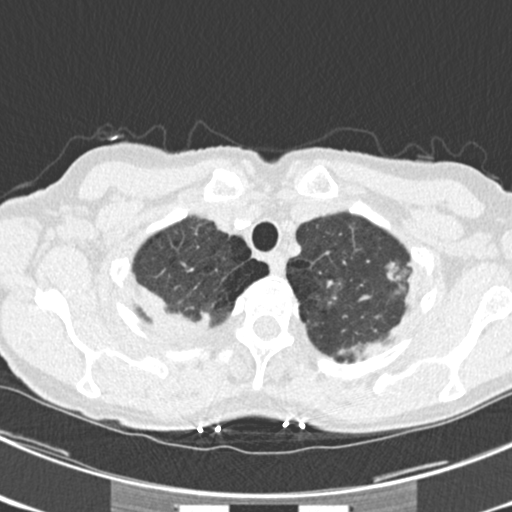
Low-dose screening chest CT, one axial slice; position 191 of 225 along the scan axis; lung window (W 1500 / L -600 HU); 2 mm slice thickness; 512 × 512 image matrix, field of view 302 × 302 mm.
Outlined on this slice (outlined manually by an expert reader):
- lesion 4 (tumor, upper lobe of right lung): box from (x=157, y=313) to (x=208, y=340) px